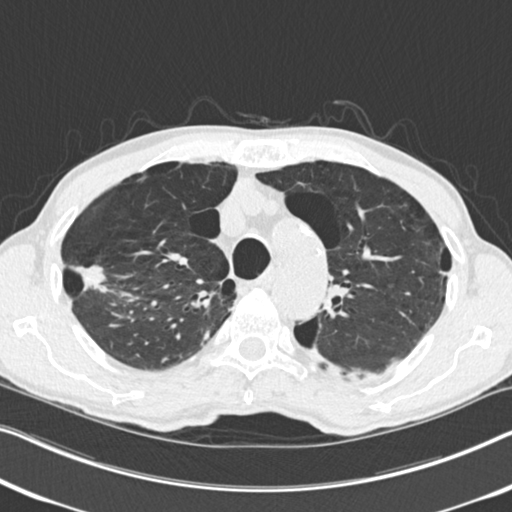
Low-dose screening chest CT, axial slice, second annual screen, lung window (W 1500 / L -600 HU), 2 mm slice thickness, standard (soft-tissue) reconstruction kernel (B30f), slice 65 of 251 in the series, 512 × 512 image matrix. Male participant, aged 71 years at enrolment.
- Expert-annotated lung lesion, bounding box <61,243,133,317> (left, top, right, bottom; pixels).
- The screening reader recorded 4 non-calcified nodules or masses ≥4 mm on this exam; which of them this box marks is not recorded.
- Official screen result: positive, change unspecified: nodule(s) >= 4 mm or enlarging nodule(s), mass(es), or other non-specific abnormalities suspicious for lung cancer.
- Lung cancer was diagnosed 83 days after this screen: adenocarcinoma, NOS, right upper lobe, well differentiated (G1), stage IA (AJCC 6th edition), 30 mm at pathology.